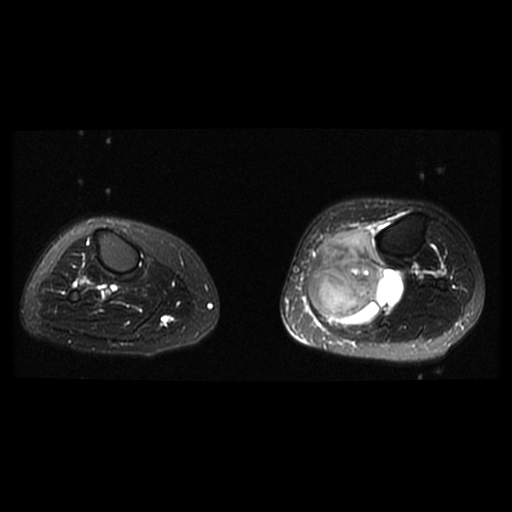
MRI of an extremity soft-tissue mass, one axial slice. Slice 18 of 38 in the series (ordered by position). T2-weighted fat-saturated. 6 mm slice thickness. 512 × 512 image matrix, field of view 330 × 330 mm. Female patient. Case-level facts recorded for this patient, not image findings: histological type: extraskeletal high grade osteogenic sarcoma; grade: high; site of the primary tumour: left calf.
Structures marked on this image (outlined manually by an expert reader):
- gross tumour volume (mass): box from (x=309, y=230) to (x=403, y=325) px